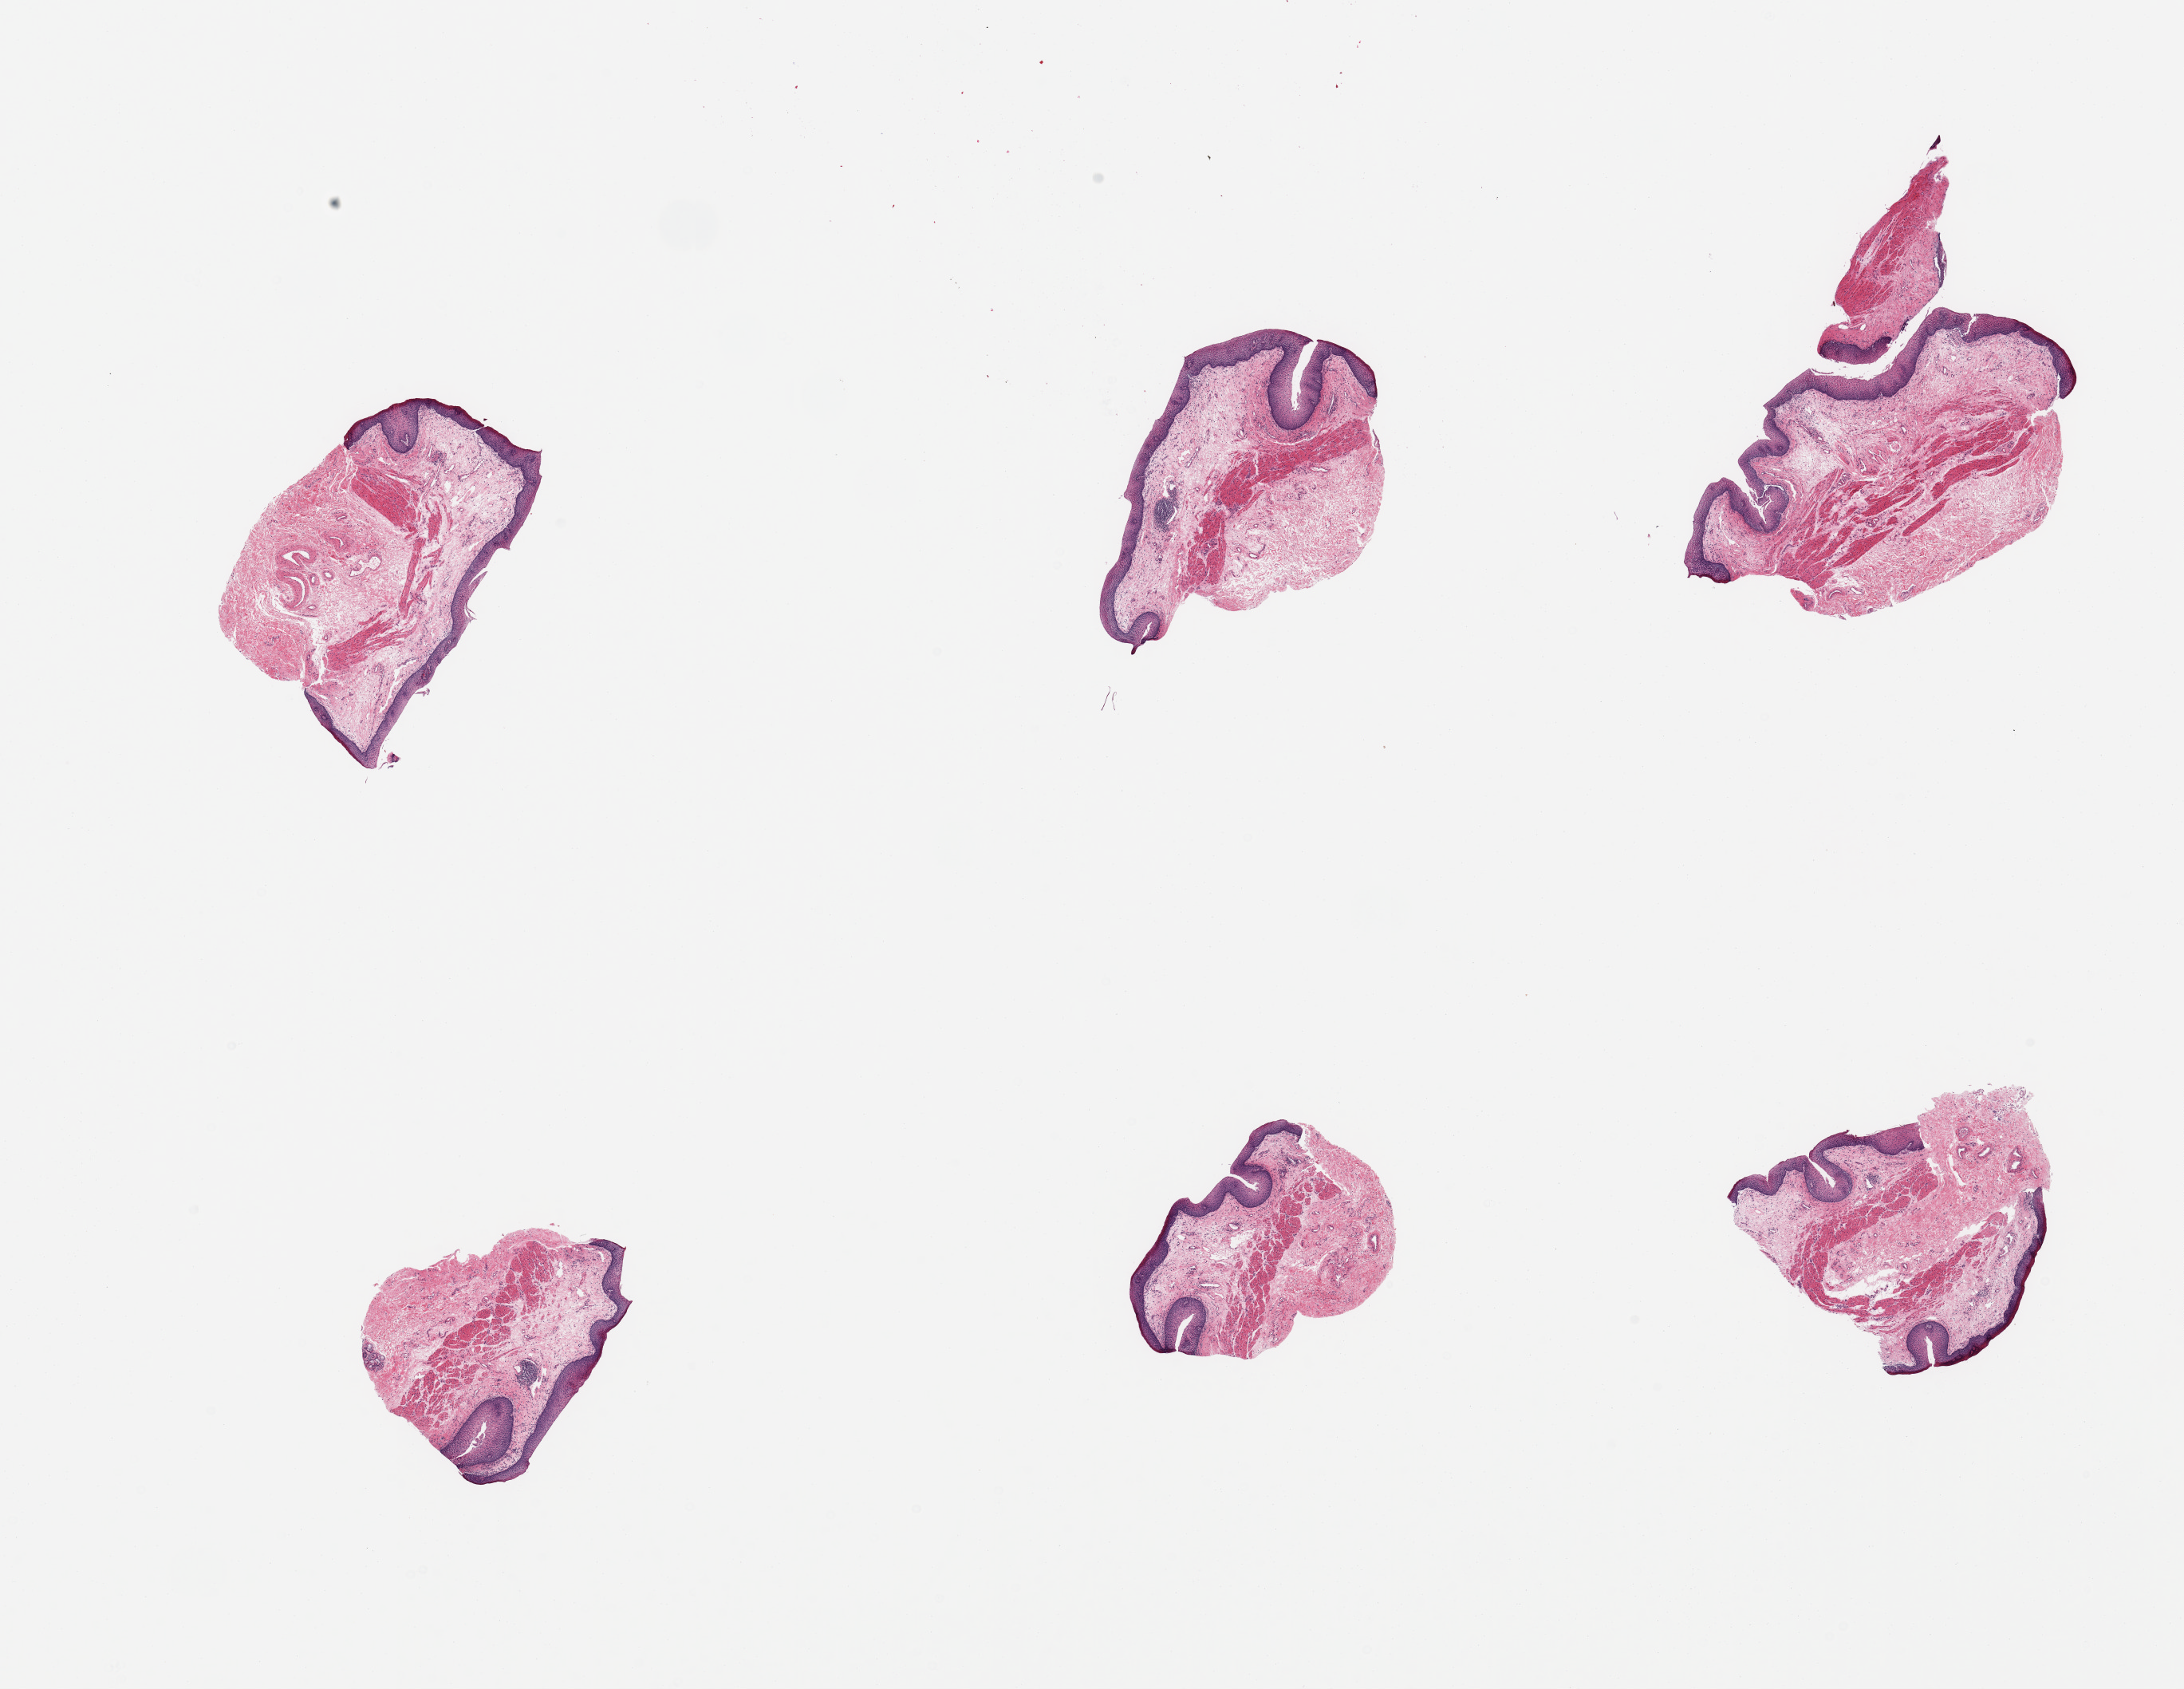
Digitized H&E-stained section, a low-resolution overview of the entire scanned area, about 21.7 x 16.7 mm; PAXgene-fixed paraffin-embedded (PFPE) section; sampled site (target tissue): esophageal mucous membrane; donor tissue sample. Donor: male.
Reviewer comment on this tissue sample: 6 pieces; patchy eosinophilic squamous surface (?irritation).